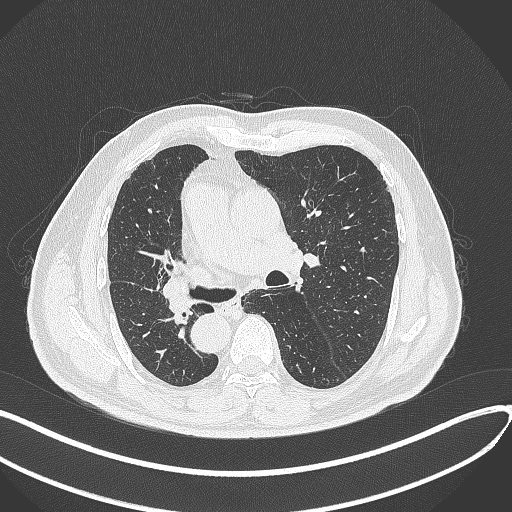
Chest CT, one axial slice. Position 164 of 300 along the scan axis. Reconstruction kernel B70f. Lung window (W 1500 / L -600 HU). 1 mm slice thickness. 512 × 512 image matrix, field of view 400 × 400 mm. Patient: male, 67 years. From the clinical record (not read from this slice): clinical TNM (as recorded): T2a N0 M0.
Annotated regions visible in this slice (rectangle marked by the reading radiologist):
- lung tumour (recorded histology: squamous cell carcinoma): bounding box [x1, y1, x2, y2] px = [162, 275, 198, 321]